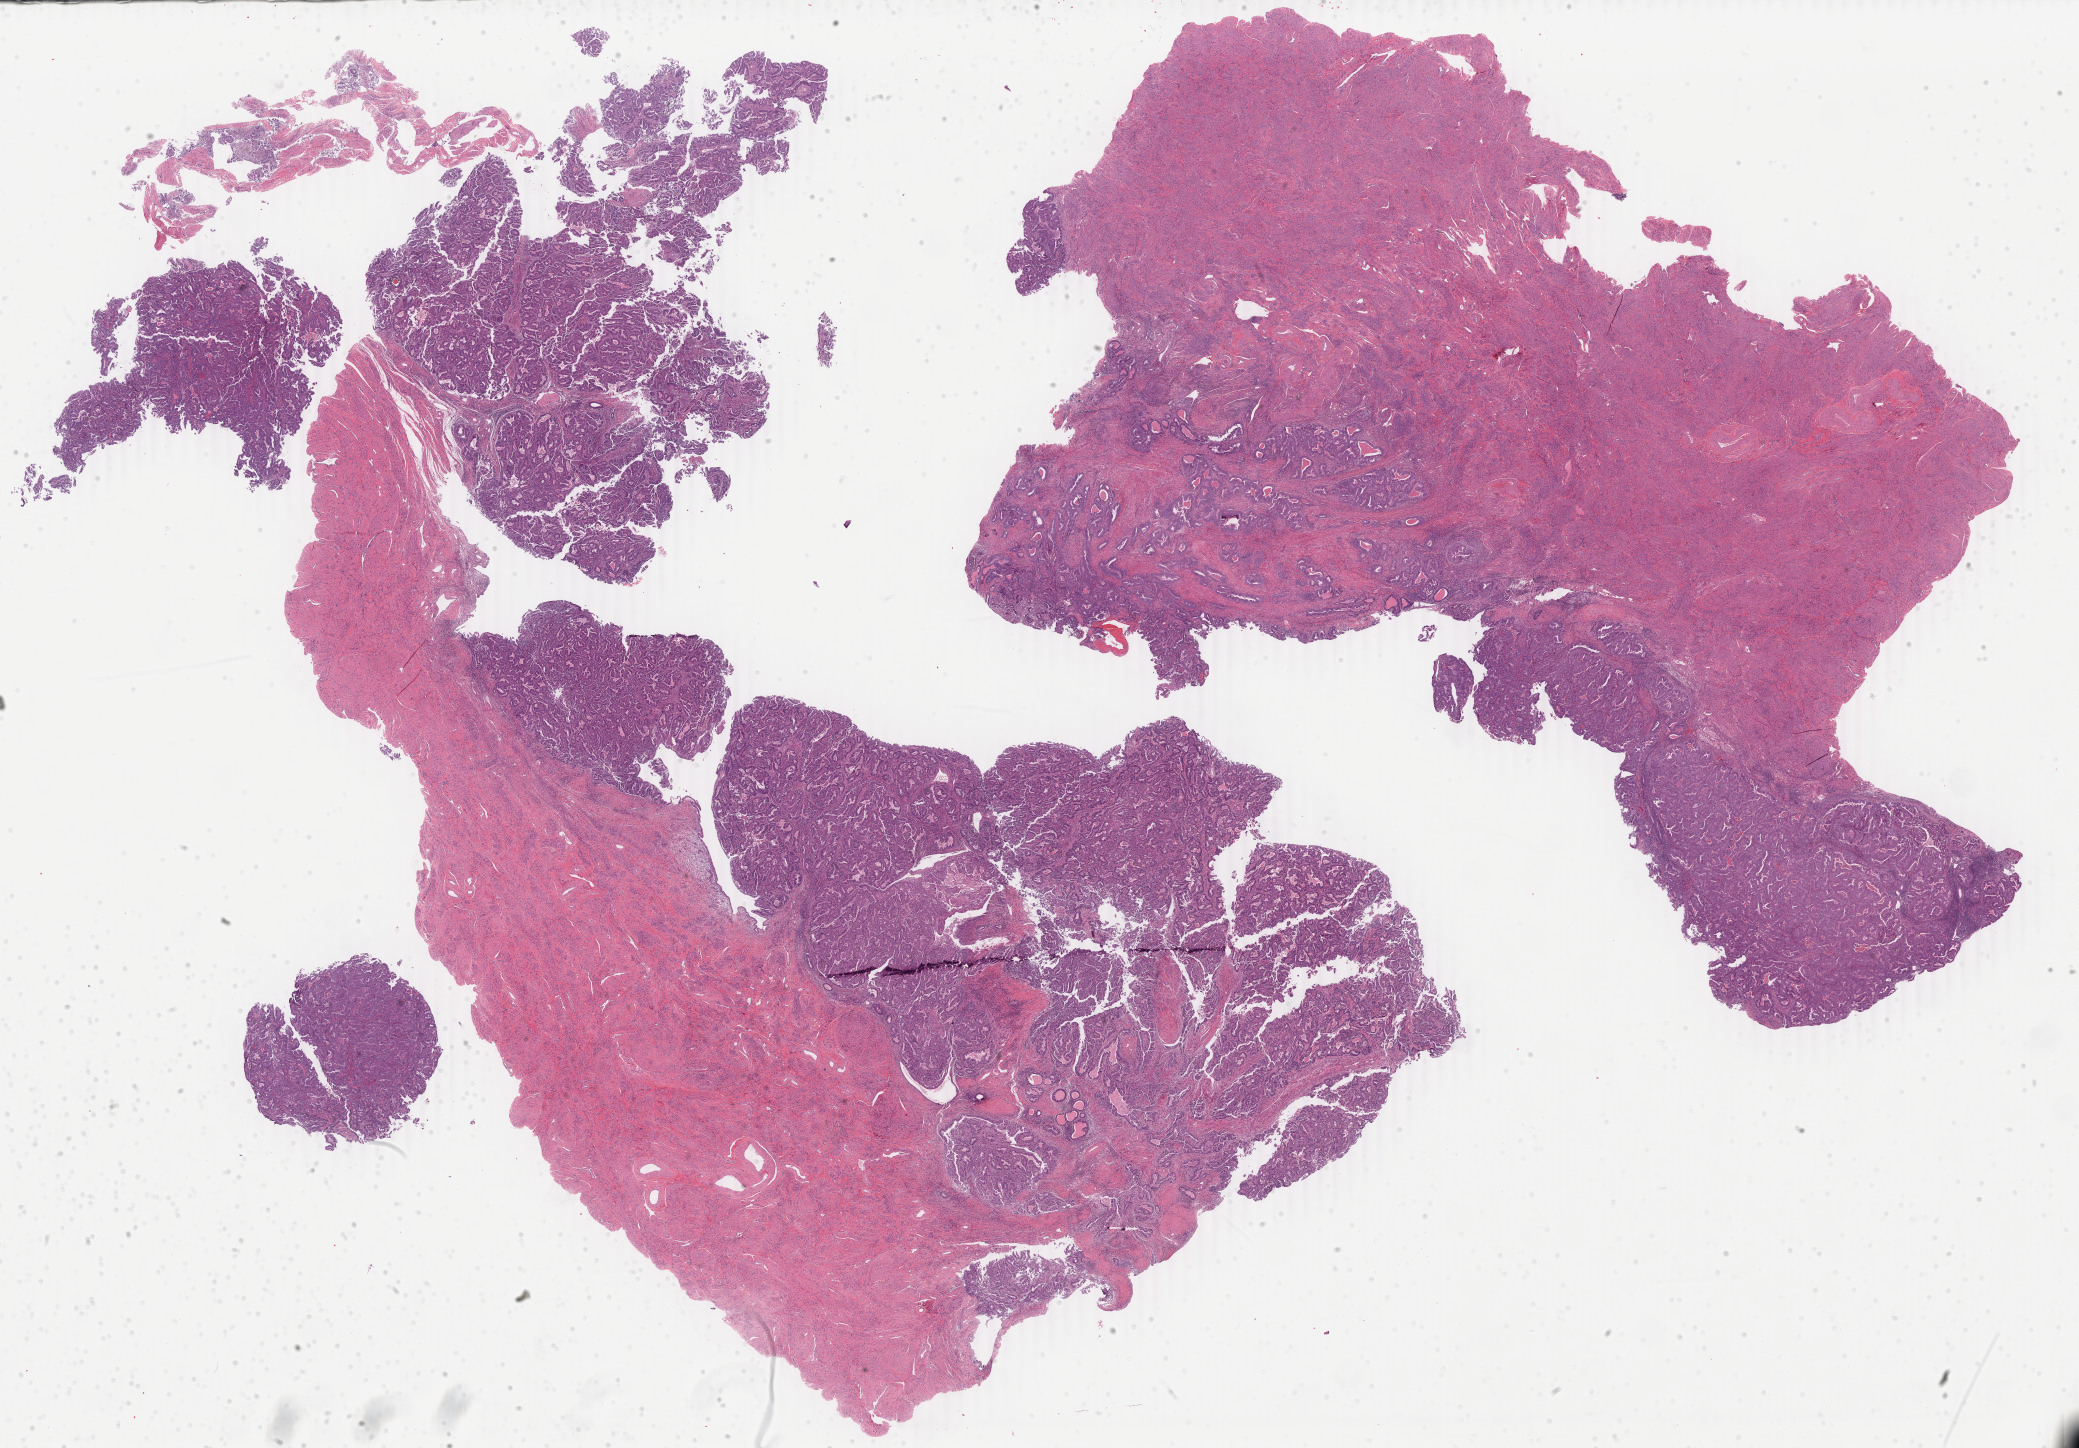
Digitized H&E-stained tissue section (whole slide) — shown as a low-resolution overview of the whole scanned area (about 33.1 x 23.0 mm, from a 40x scan). Formalin-fixed paraffin-embedded (FFPE) diagnostic section. Sample: primary tumour, uterus. Female patient; age at initial diagnosis 49 years.
Diagnosis: Endometrioid adenocarcinoma, NOS.